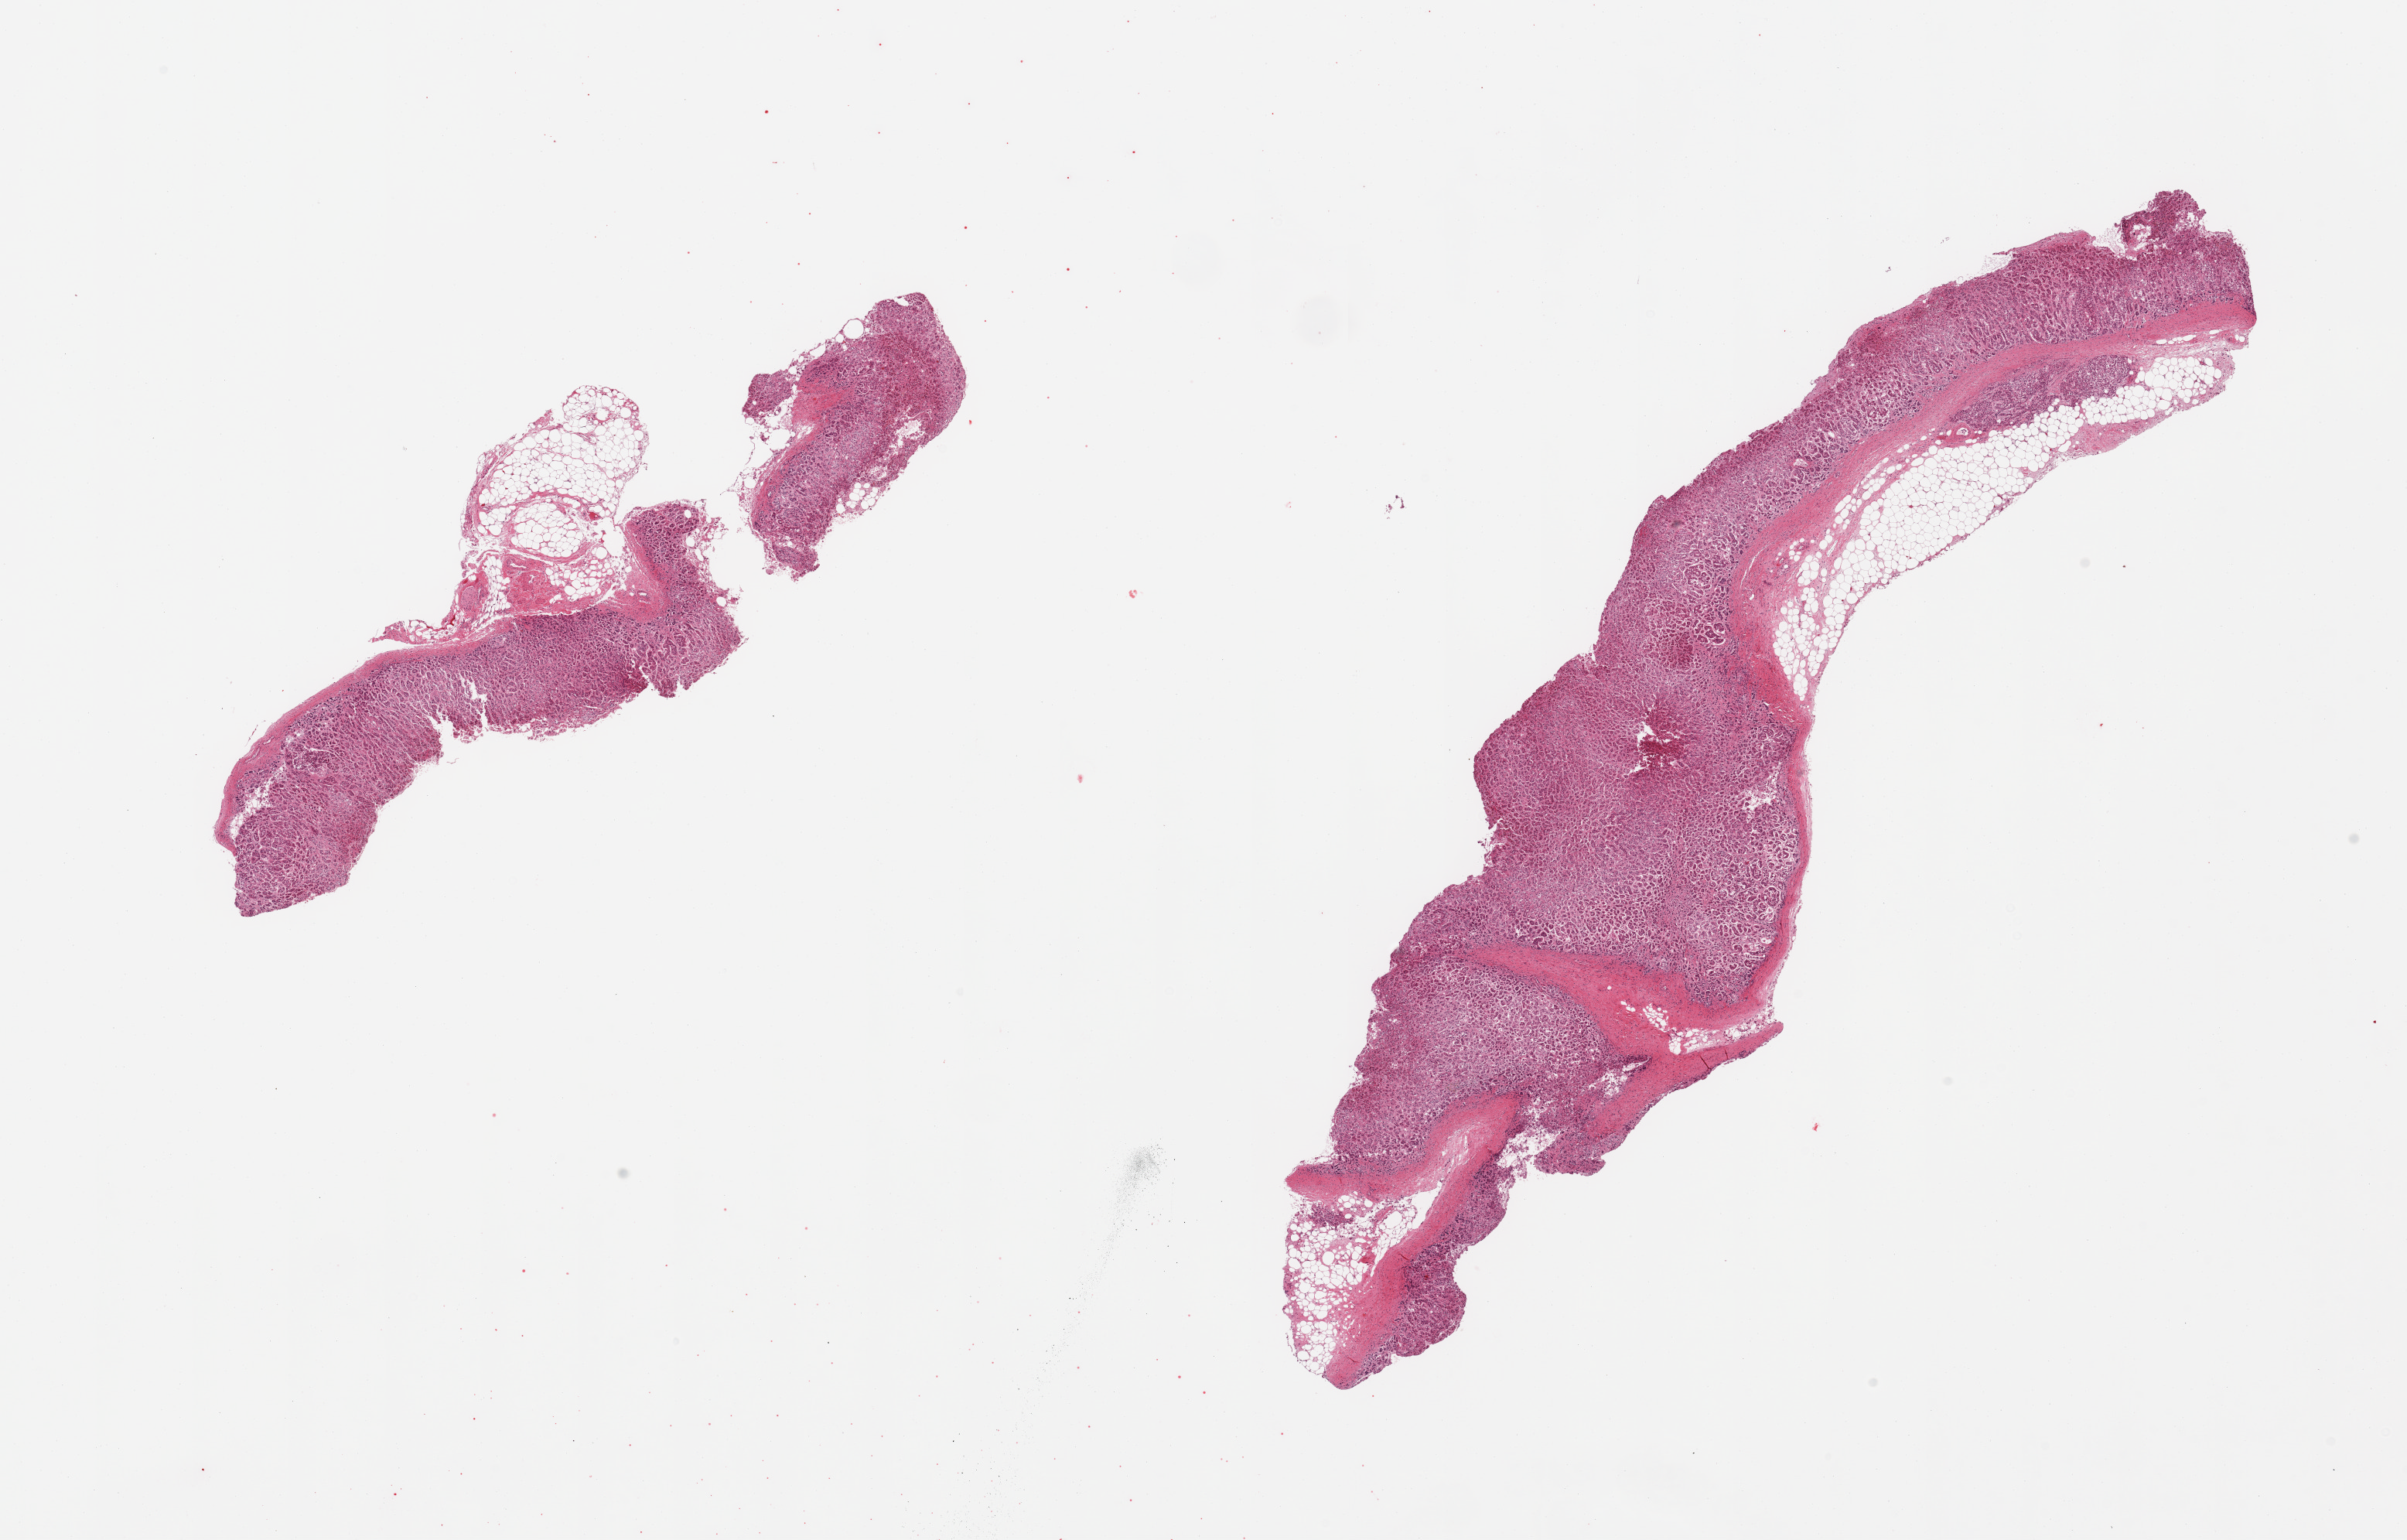
Digitized hematoxylin and eosin (H&E)-stained section, whole scanned area (about 24.6 x 15.7 mm) shown as a low-resolution overview; PAXgene-fixed, paraffin-embedded tissue; section of adrenal gland (target tissue); donor tissue sample. Female donor.
- reviewer comment on this tissue sample: 2 pieces; 25% external fat